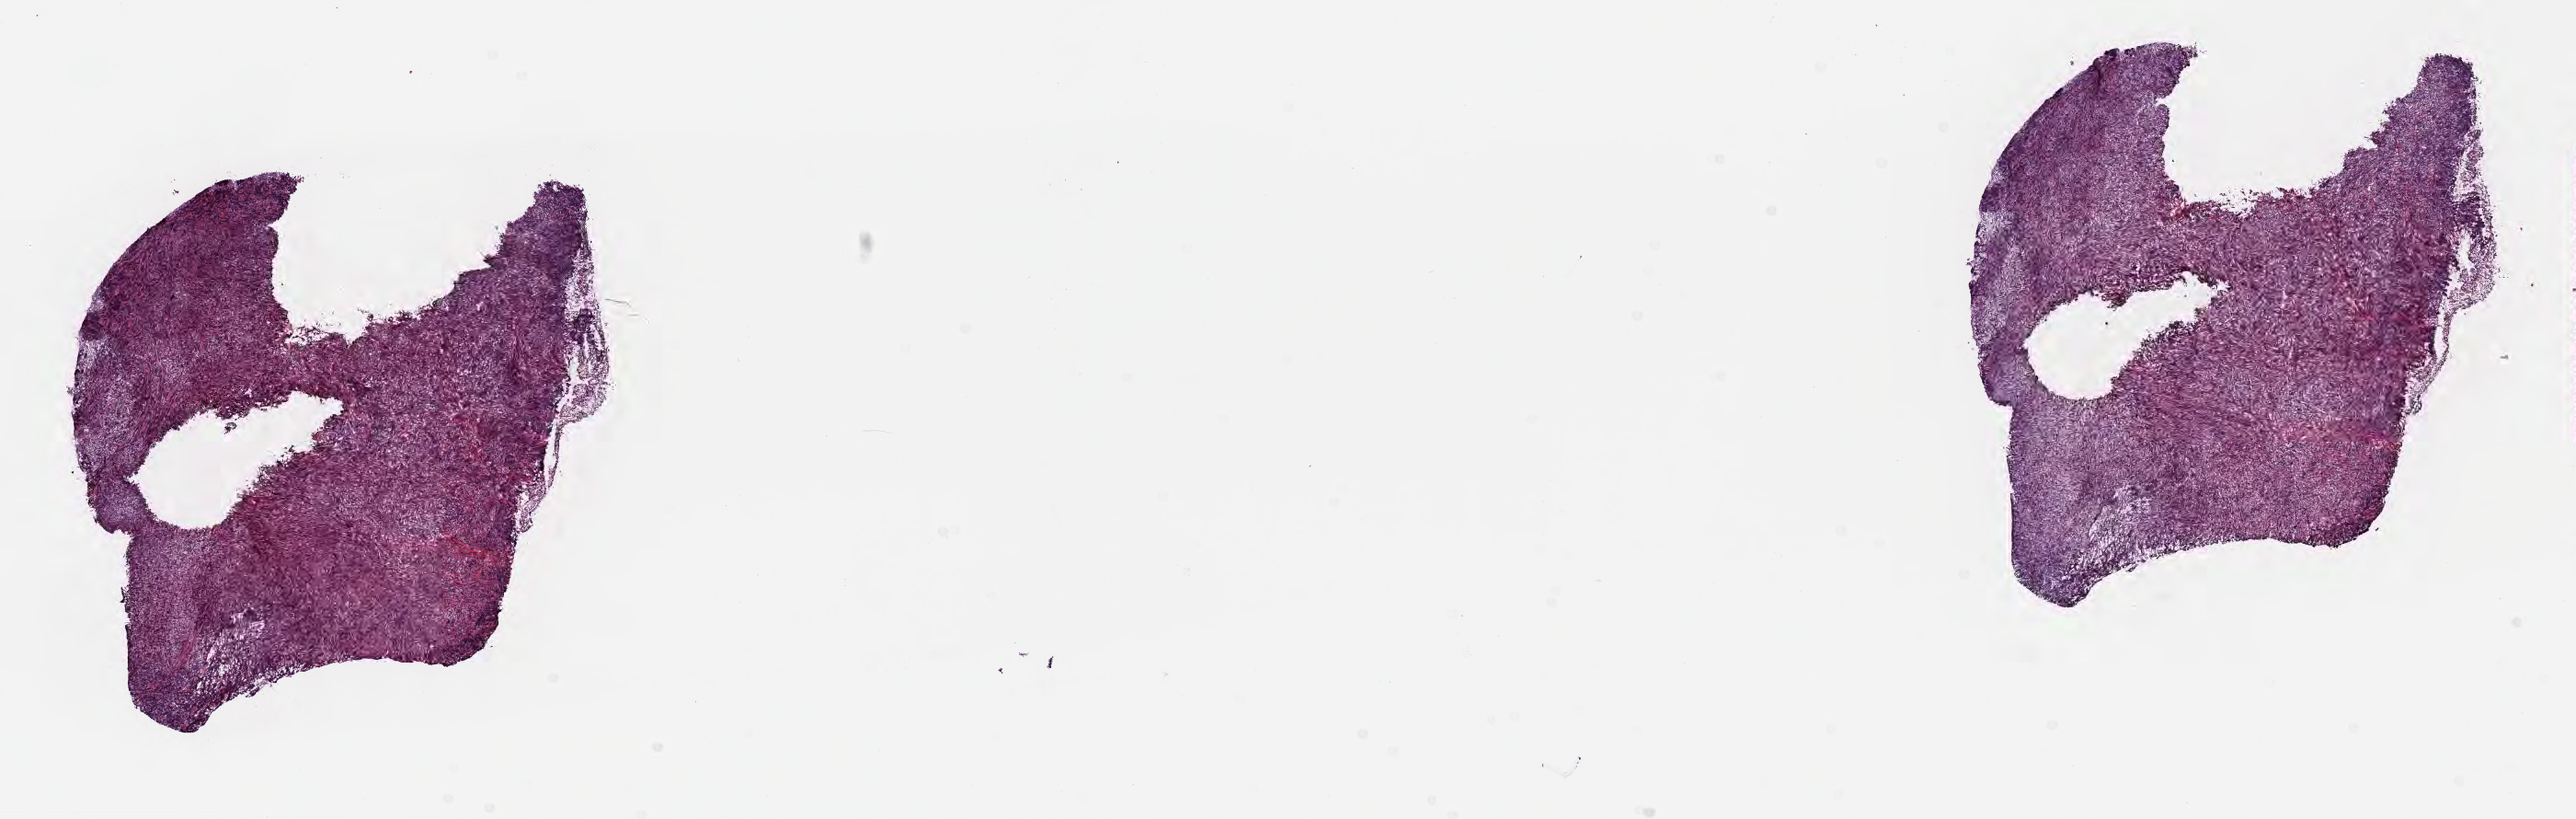
Hematoxylin and eosin (H&E) whole-slide image, whole scanned area (about 22.7 x 7.2 mm) shown as a low-resolution overview, frozen section (tissue freezing medium), specimen: primary tumor, anatomic site: mandible. Female, age 7 years at initial diagnosis.
Diagnosis: Burkitt lymphoma, NOS.